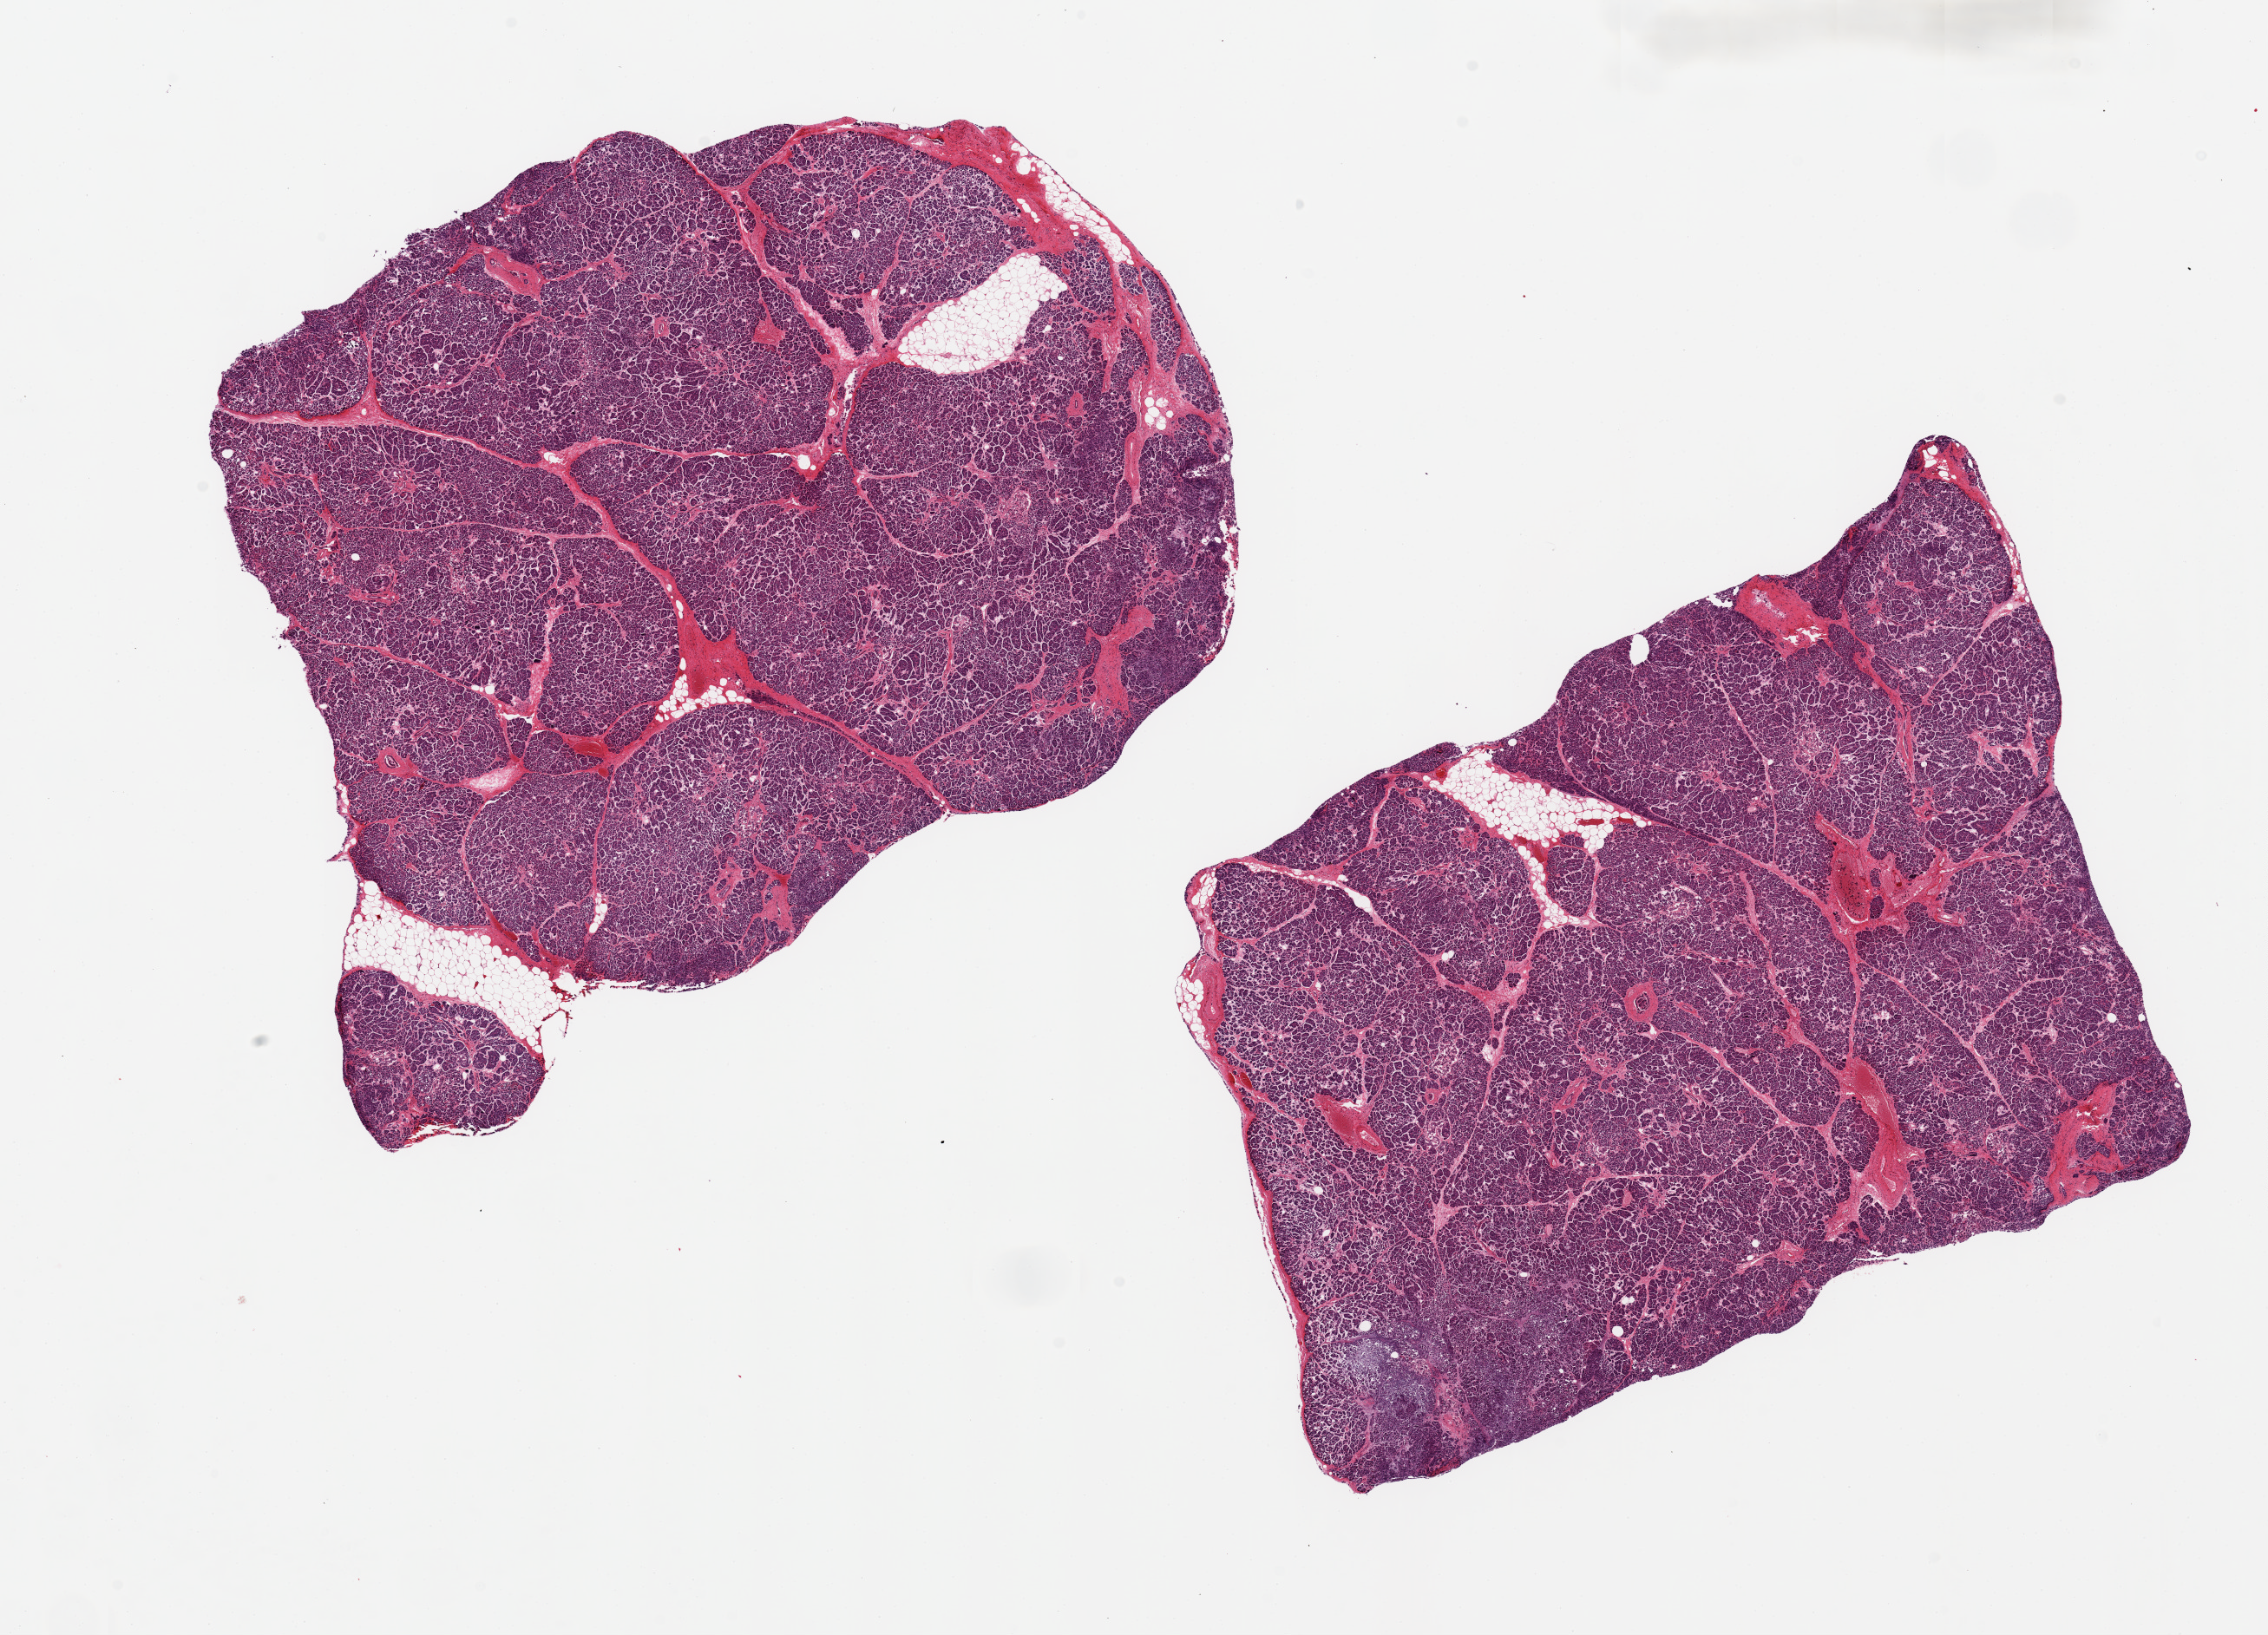
Whole-slide image, H&E stain, brightfield — shown as a low-resolution overview of the whole scanned area (about 20.7 x 14.9 mm, from a 20x scan), PAXgene-fixed paraffin-embedded (PFPE) section, target tissue: pancreas, donor tissue sample.
Review note (as recorded): 2 pieces ~8x7mm; Islets more badly autolyzed; a few.